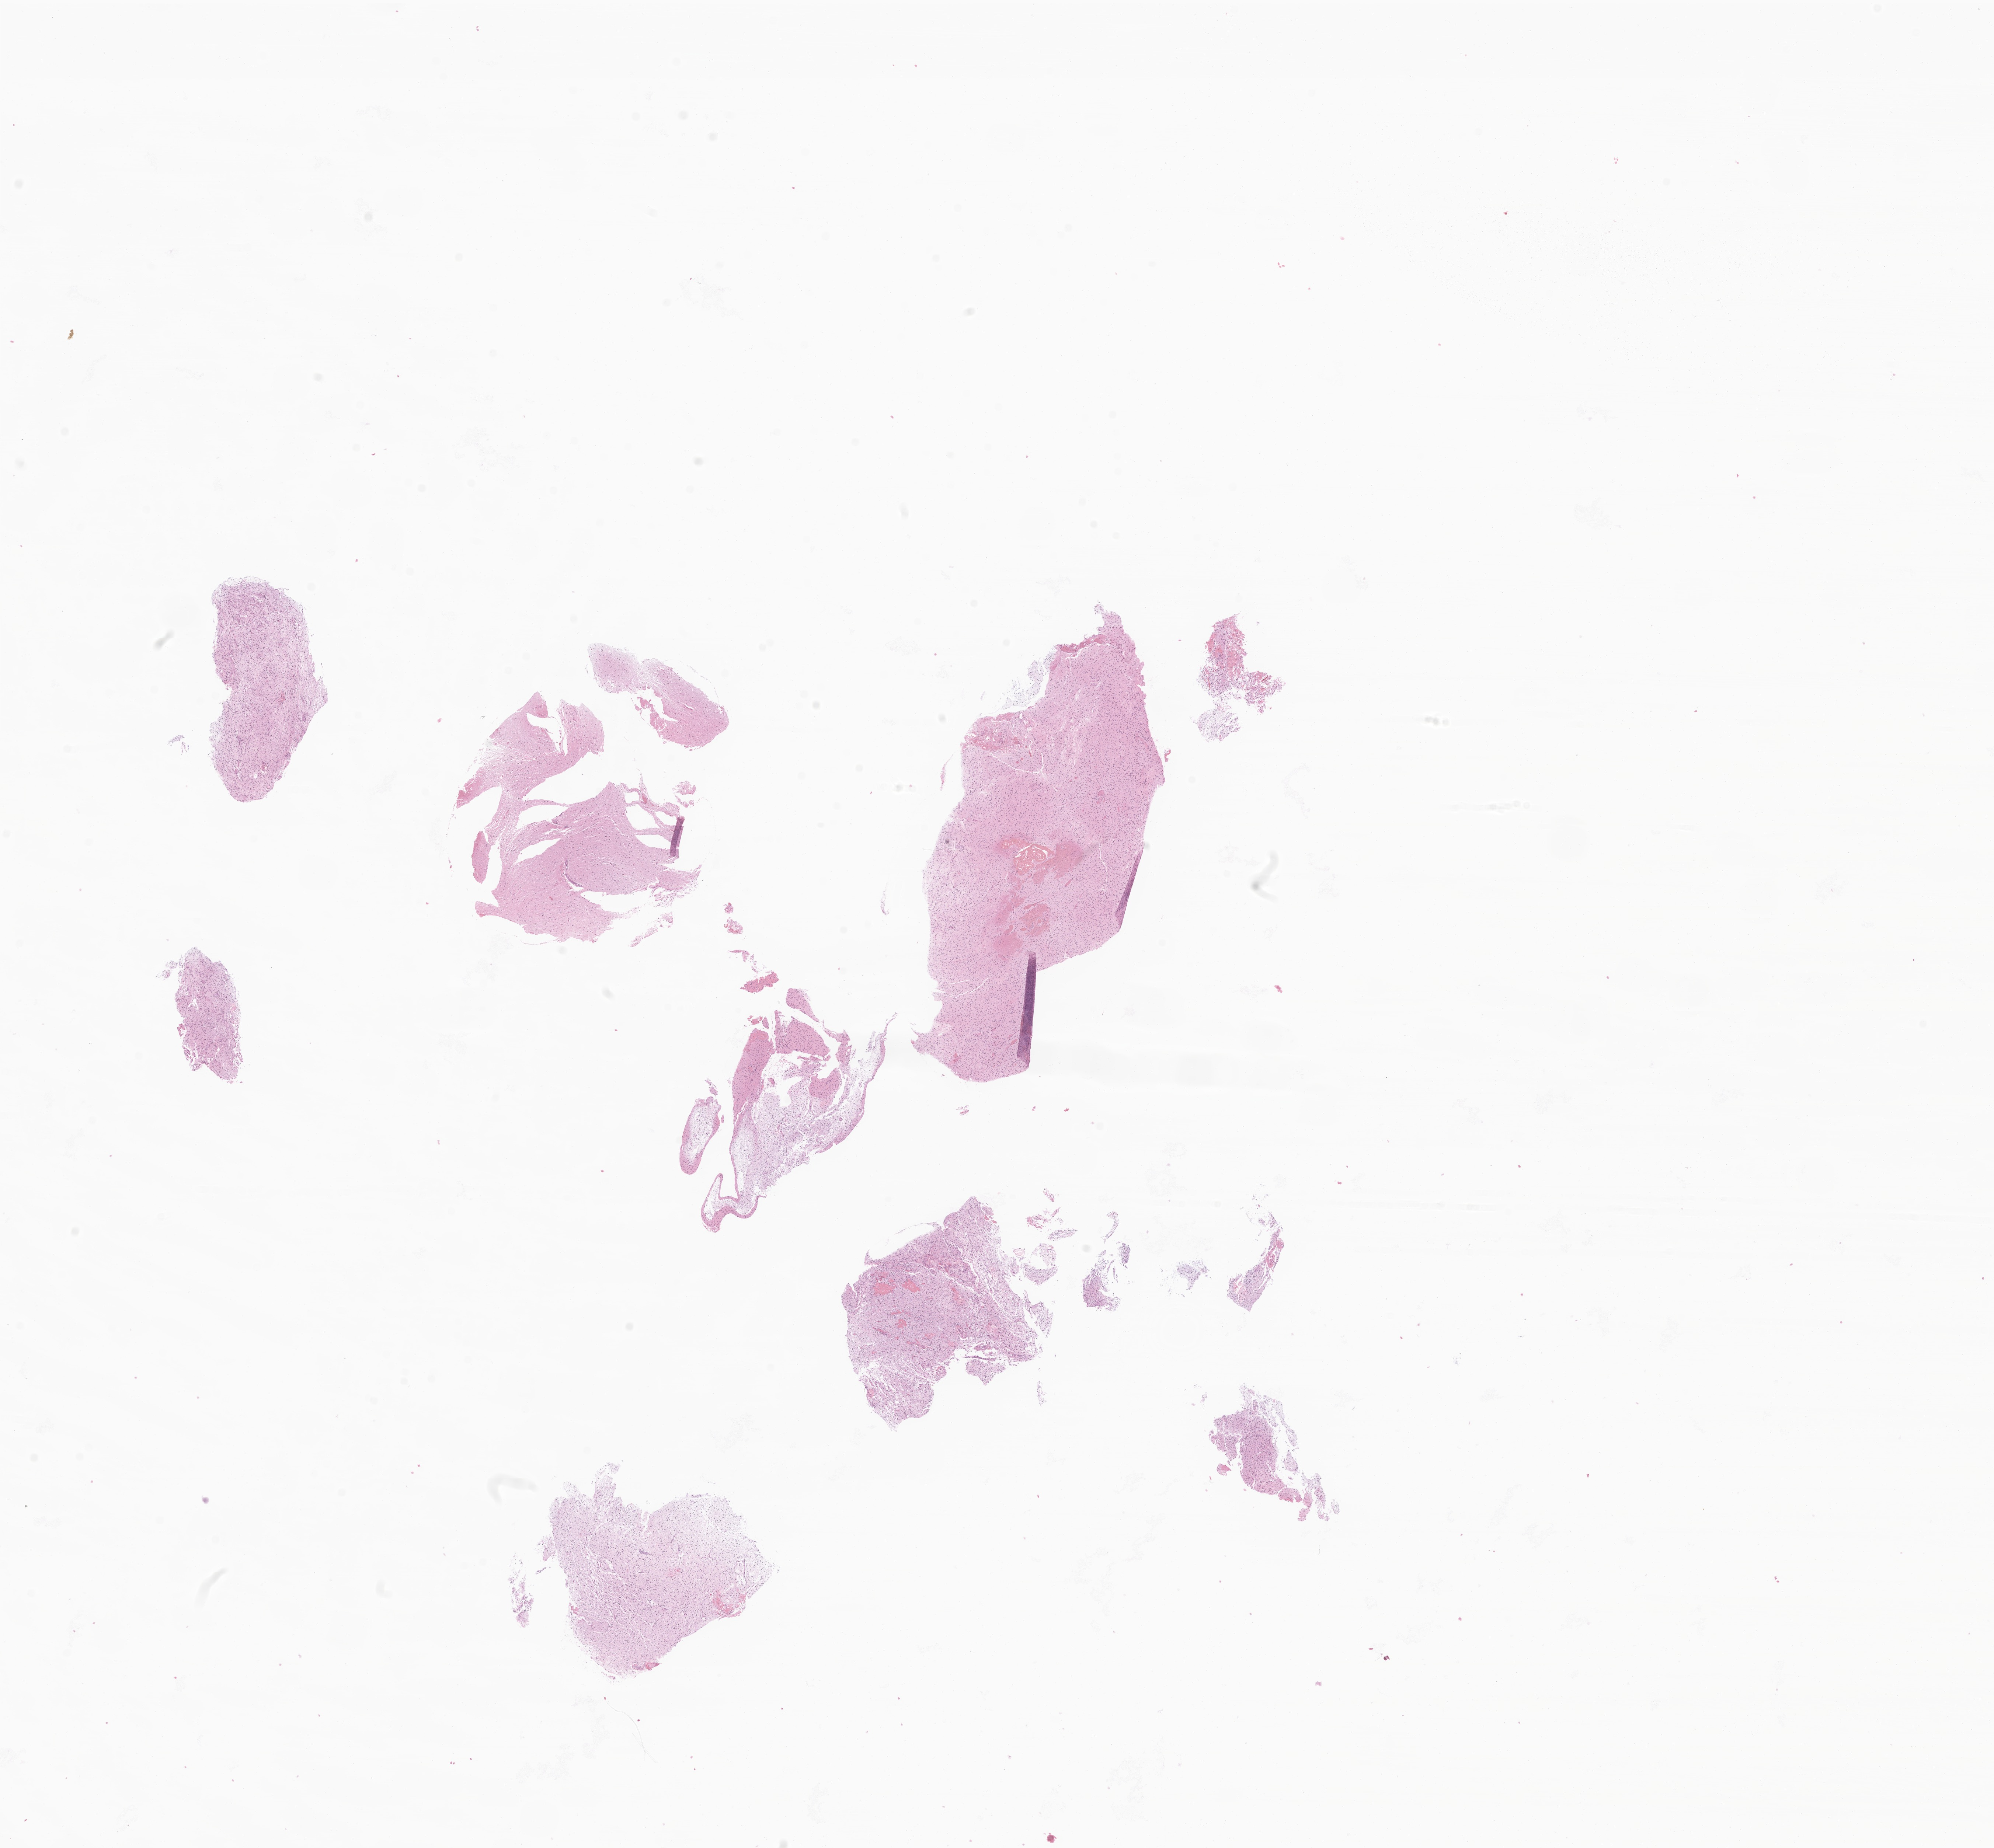
Whole-slide image, hematoxylin and eosin (H&E) stain of tumor tissue from the brain, a low-resolution overview of the entire scanned area, about 22.8 x 21.1 mm. Formalin-fixed paraffin-embedded section. Patient: female, age 128 months (10 years 8 months).
• diagnosis (ICD-O-3 morphology term): Pilocytic astrocytoma